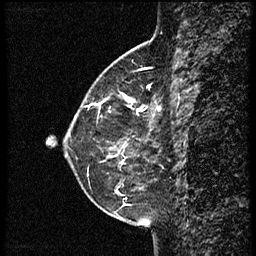
Breast MRI (dynamic contrast-enhanced), one sagittal slice. Slice 20 of 60 in the series (ordered by position). Dynamic contrast-enhanced study with each time point stored as its own series, time point 2 of 3 at this slice position (early post-contrast, ordered by acquisition time). 1.5 T. TE 4.2 ms, TR 18.9 ms. 2 mm slice thickness. 256 × 256 image matrix, field of view 200 × 200 mm. Female patient. Case-level facts recorded for this patient, not image findings: setting: breast cancer imaged before/during neoadjuvant chemotherapy; receptor status: HER2-positive.
Structures marked on this image (semi-automatic segmentation, software-assisted and operator-edited):
- analysis volume of interest (the breast-tissue region the enhancement analysis was run in; not a lesion): bounding box [x1, y1, x2, y2] px = [77, 69, 161, 147]
- tumour enhancement mask (voxels above the 100 % enhancement threshold inside the analysis volume of interest): [93, 99, 161, 110]